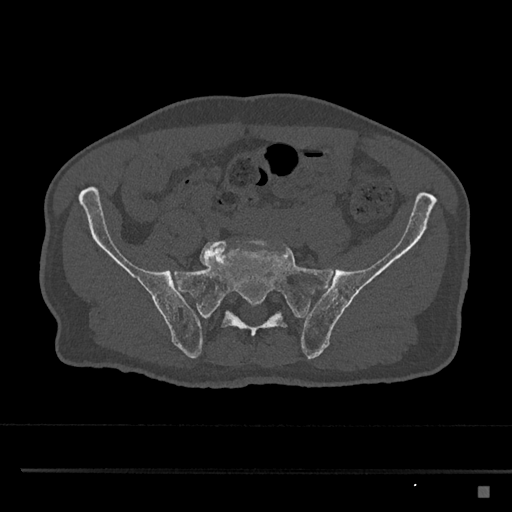
CT including the spine, one axial slice; position 527 of 797 along the scan axis; reconstruction kernel Br40s/3; 120 kVp; bone window (W 1800 / L 400 HU); 0.5 mm slice thickness; 512 × 512 image matrix, field of view 391 × 391 mm. Male patient, age 59 years. From the clinical record (not read from this slice): primary cancer: prostate.
Structures marked on this image (semi-automatically segmented with operator editing):
- L5 vertebra: bounding box (x1, y1, x2, y2) in pixels: (199, 238, 270, 267)